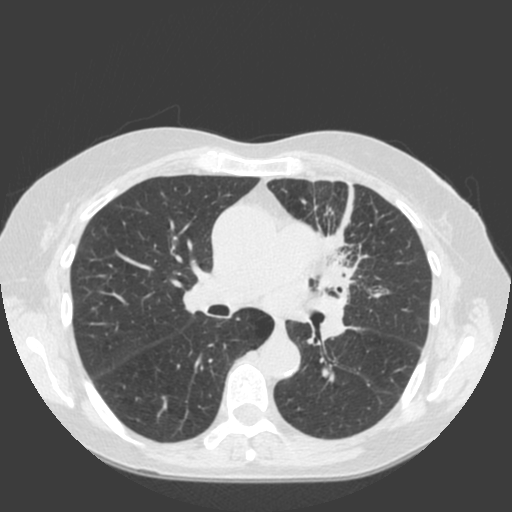
Low-dose screening chest CT, axial slice. First (baseline) screen. Lung window (W 1500 / L -600 HU). Standard (soft-tissue) reconstruction kernel (C). Slice 74 of 184 in the series. Female, age 66 years at enrolment. Current smoker at enrolment.
Expert-annotated lung lesion, bounding box (x1, y1, x2, y2) in pixels: (276, 201, 402, 315). The exam's reader record, not a measurement of the box and not confirmed to be the same lesion: non-calcified nodule or mass ≥4 mm, left upper lobe, 61 × 45 mm, spiculated (stellate) margins, soft tissue attenuation.